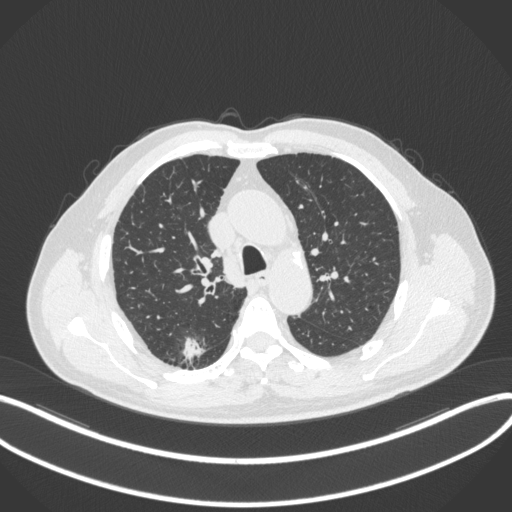
Chest CT, one axial slice; position 261 of 366 along the scan axis; 120 kVp; lung window (W 1500 / L -600 HU); 512 × 512 image matrix, field of view 400 × 400 mm. Patient: male, 69 years. Case-level facts recorded for this patient, not image findings: clinical TNM (as recorded): T1b N0 M0; histopathological grade: G2-3.
Outlined on this slice (bounding box drawn by a radiologist):
- lung tumour (recorded histology: adenocarcinoma): box from (x=179, y=334) to (x=208, y=364) px